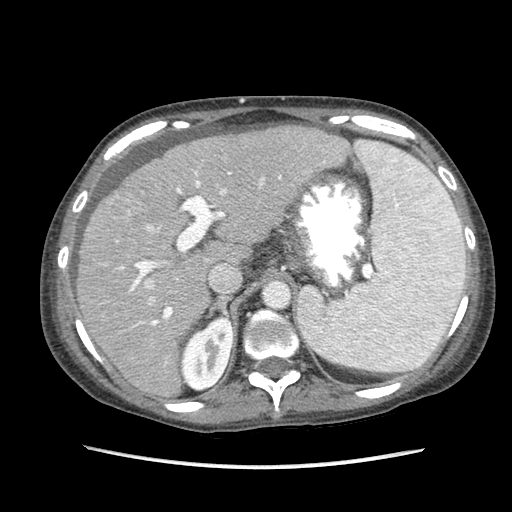
Contrast-enhanced abdominal CT (liver protocol), one axial slice. Slice 59 of 87 in the series (ordered by position). 120 kVp. Soft-tissue window (W 400 / L 40 HU). 512 × 512 image matrix. From the clinical record (not read from this slice): diagnosis: hepatocellular carcinoma (patient treated with transarterial chemoembolisation; whether this scan precedes or follows treatment is not stated here); TNM stage (as recorded): Stage-IIIB; Child-Pugh class: A; tumour differentiation: no biopsy.
Structures marked on this image (semi-automatic segmentation, software-assisted and operator-edited):
- abdominal aorta: box from (x=264, y=282) to (x=289, y=308) px
- liver parenchyma outside the tumour (the mass and vessels are separate outlines, so this box may not span the whole liver): (x=76, y=125)–(x=349, y=396)
- mass: (x=105, y=195)–(x=131, y=220)
- liver vessels: (x=117, y=161)–(x=325, y=365)